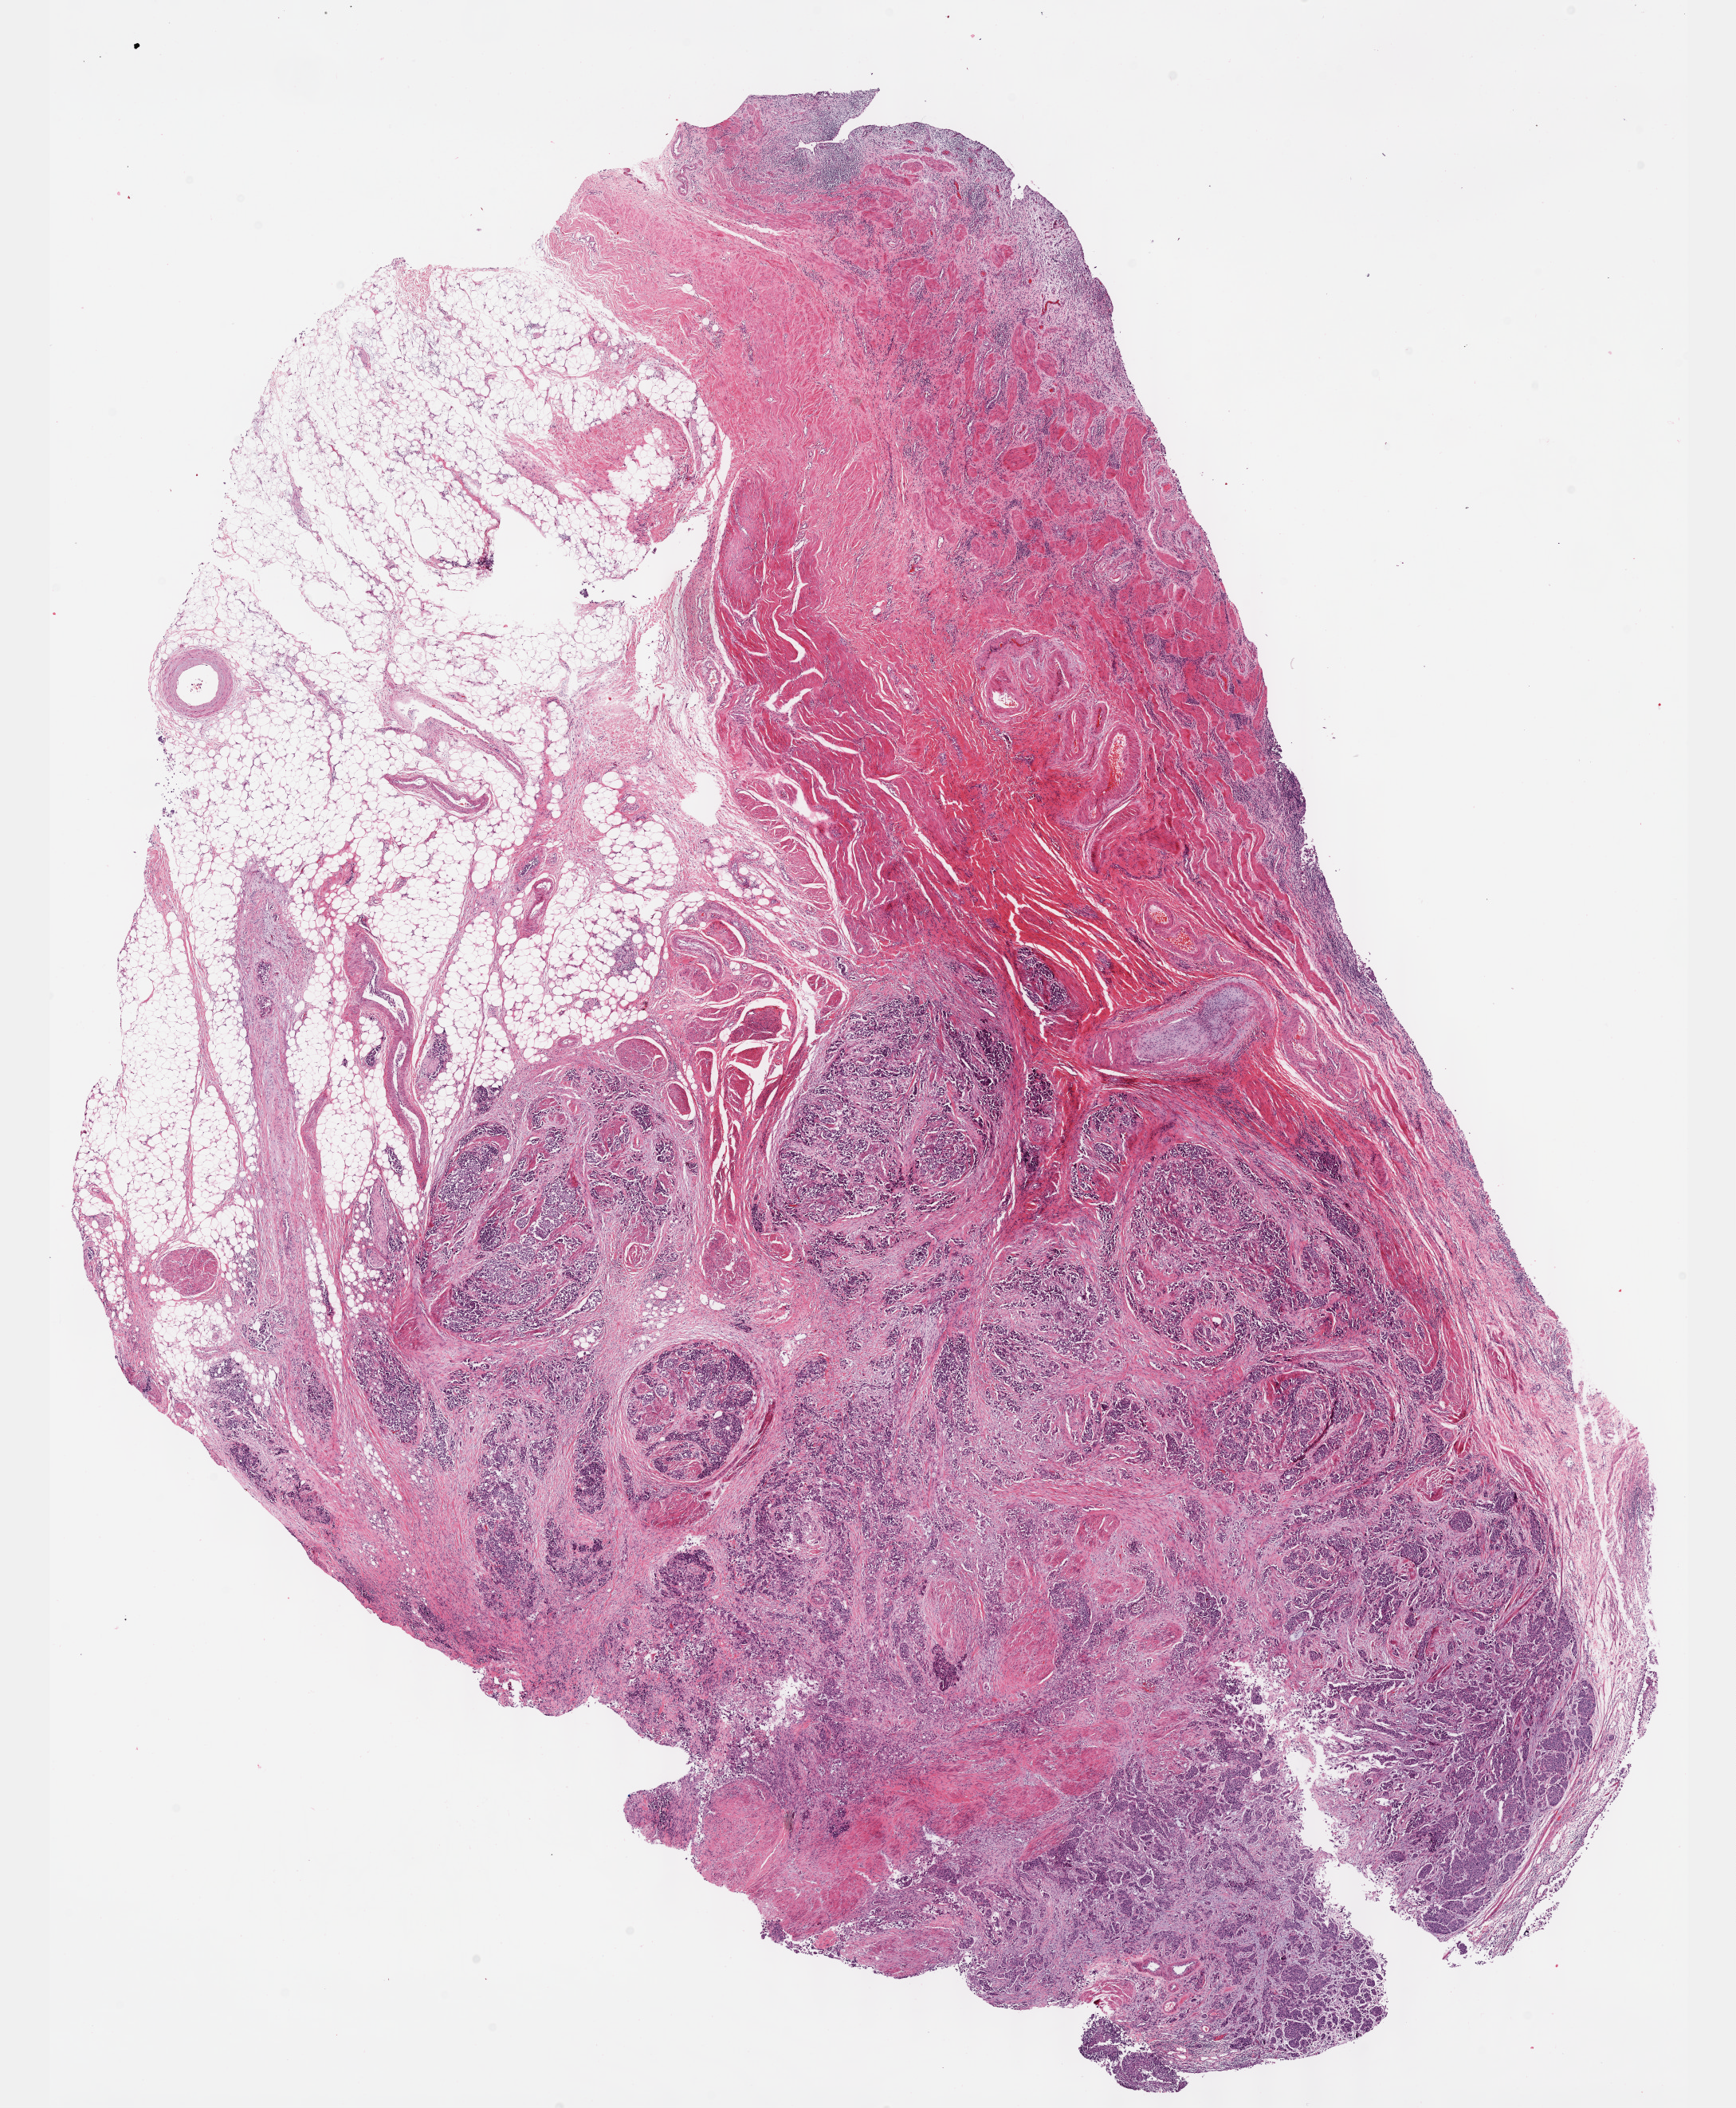
Digitized H&E-stained tissue section (whole slide), low-resolution overview of the scanned area, about 17.6 x 21.4 mm; formalin-fixed paraffin-embedded (FFPE) diagnostic section; primary tumour sample from the bladder. Male, age 81 years at initial diagnosis. Histologic grade: high grade.
* AJCC pathologic stage: IV (7th edition)
* lymph nodes positive (case pathology): 3 of 6 examined
* histologic diagnosis: Transitional cell carcinoma
* TNM: T3b N2 MX